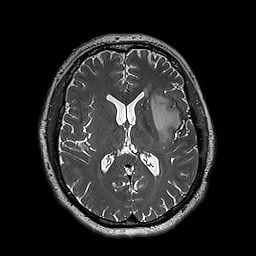
Brain MRI from a brain-tumour surgery series, one axial slice. Slice 96 of 192 in the series (ordered by position). 1 mm slice thickness. 256 × 256 image matrix, field of view 250 × 250 mm. From the clinical record (not read from this slice): histopathology: Astrocytoma; WHO grade: 3; IDH mutation: yes; tumour location: Left Insular.
Structures marked on this image (manually delineated by an expert):
- tumour: box from (x=151, y=94) to (x=182, y=144) px